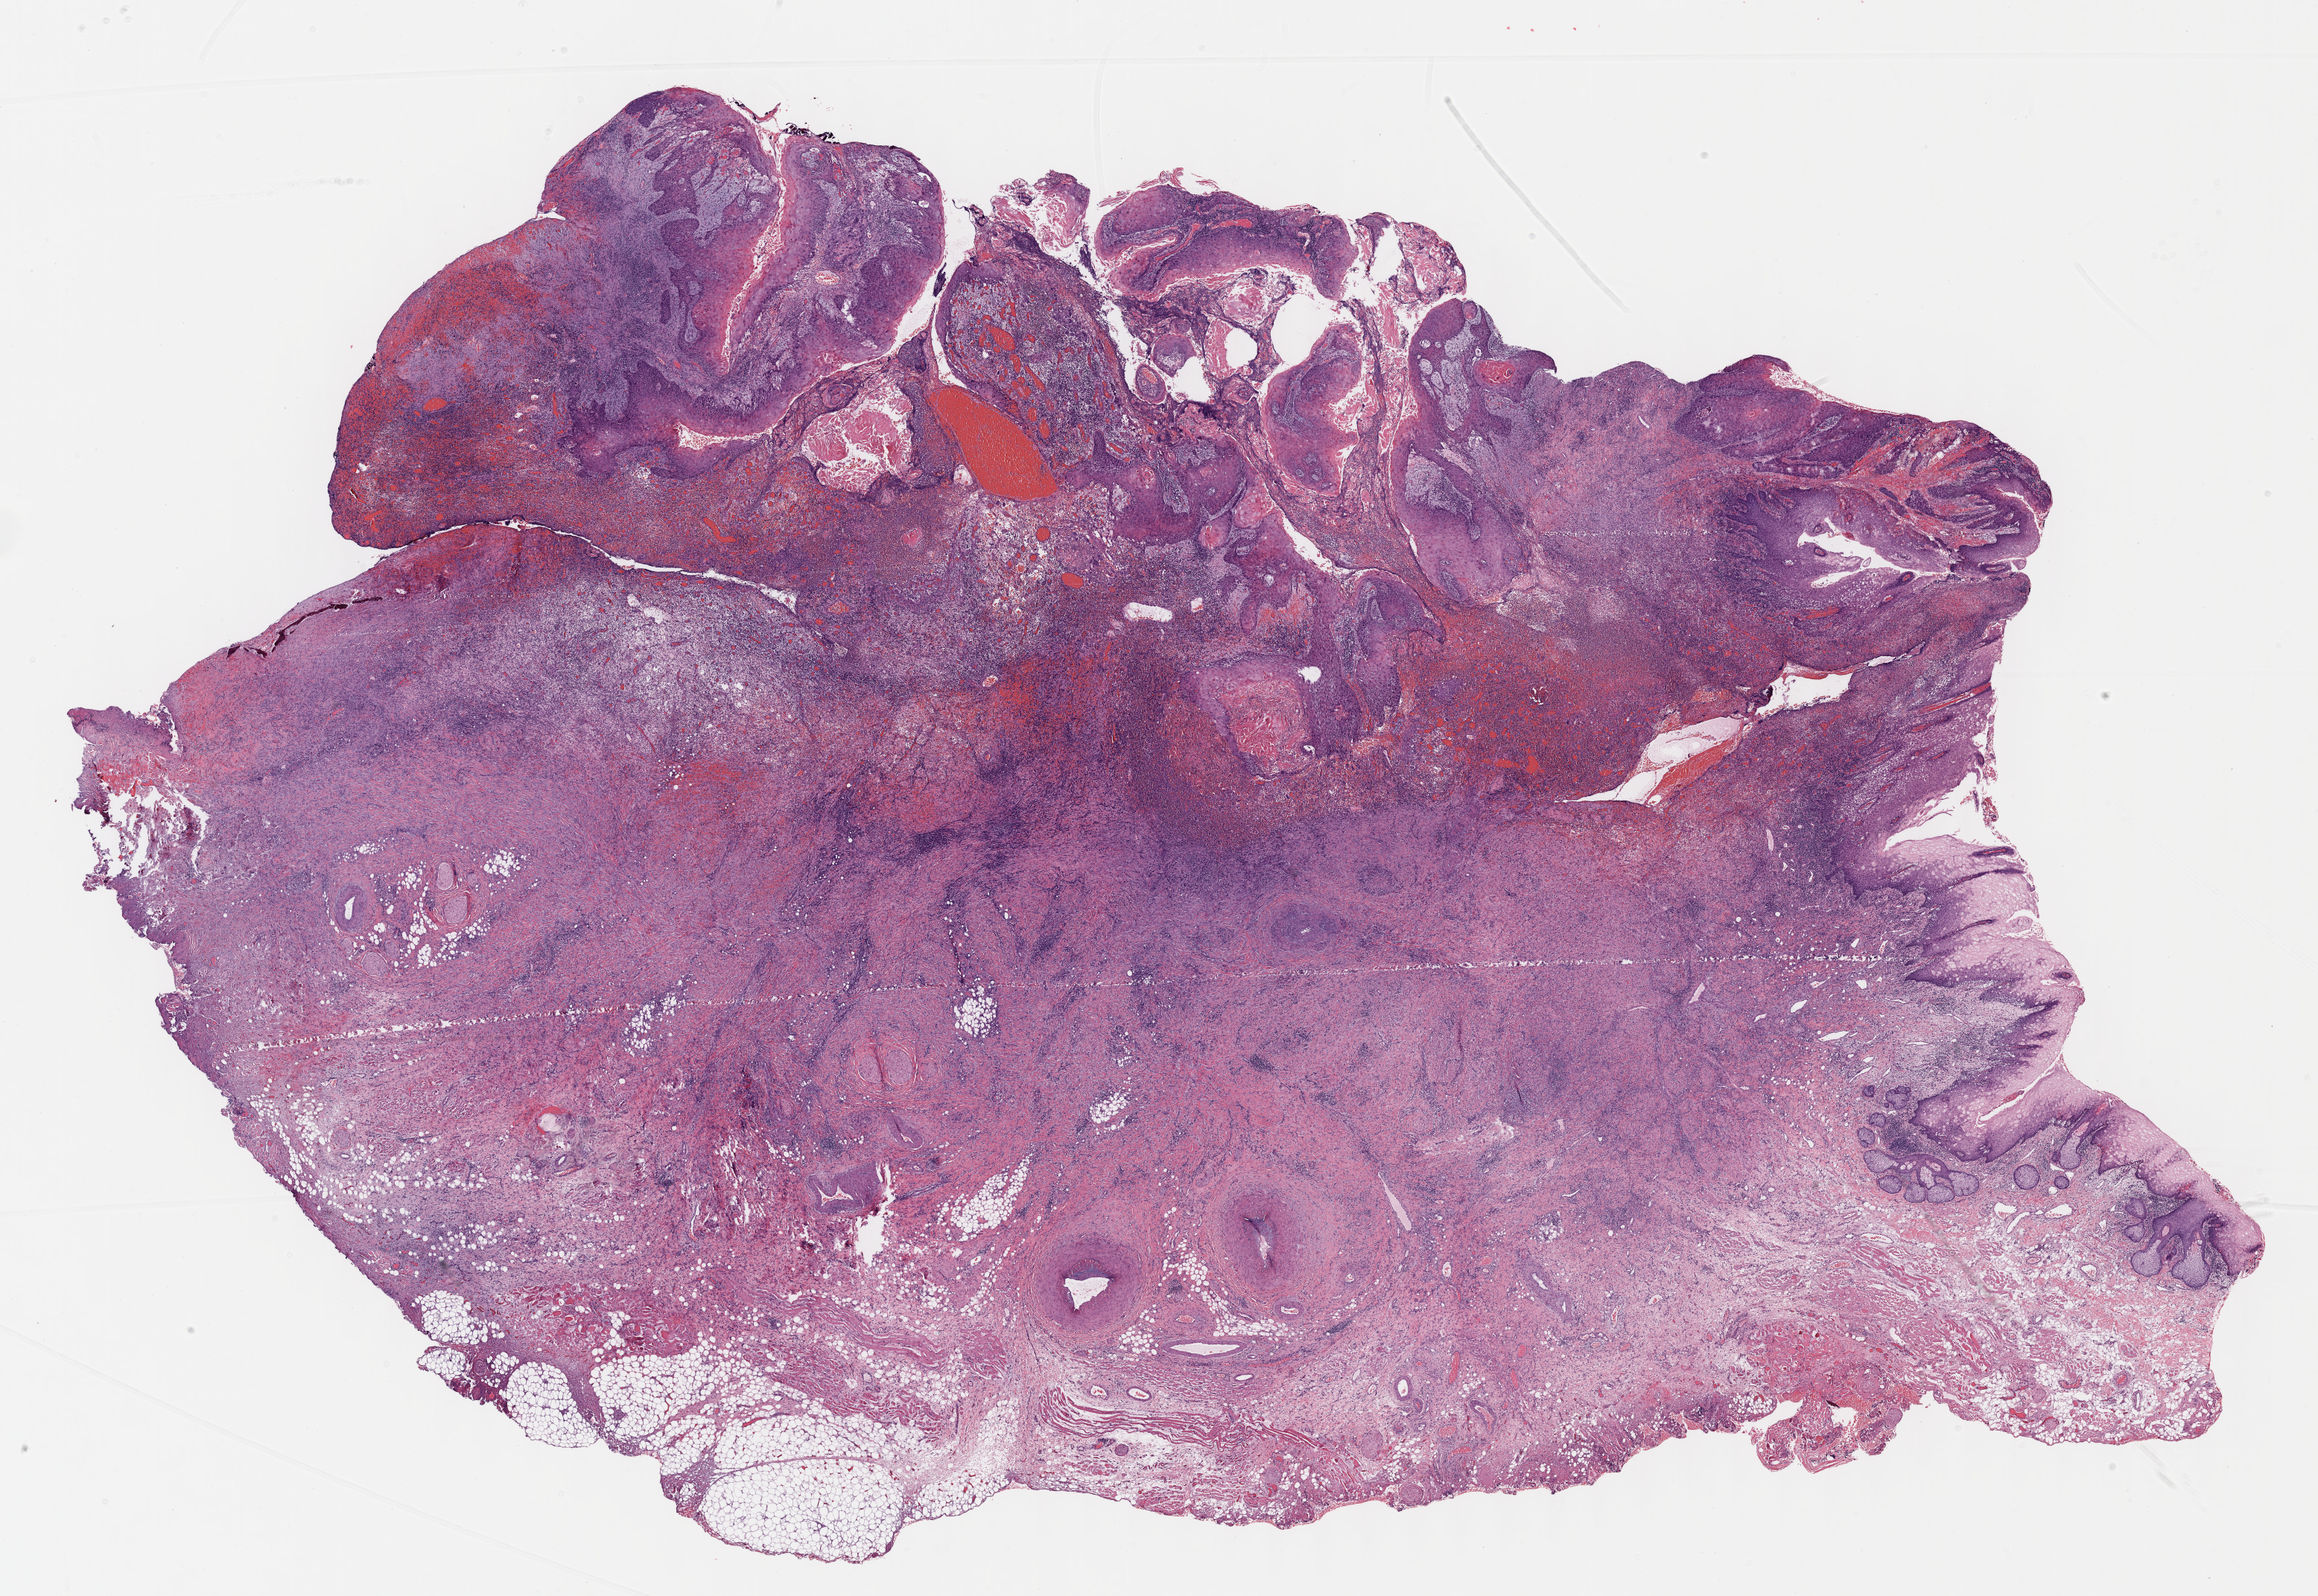
Digitized Hematoxylin and eosin (H&E) stained tissue section (whole slide), shown as a low-resolution overview of the whole scanned area (about 25.1 x 17.3 mm); formalin-fixed paraffin-embedded (FFPE) diagnostic section; head and neck, primary tumour sample. Patient: male, age at initial diagnosis 69 years. Histologic grade: G1 (well differentiated).
• TNM: T4a N0 M0
• diagnosis: Squamous cell carcinoma, NOS (mouth, NOS)
• AJCC pathologic stage: IVA (7th edition)